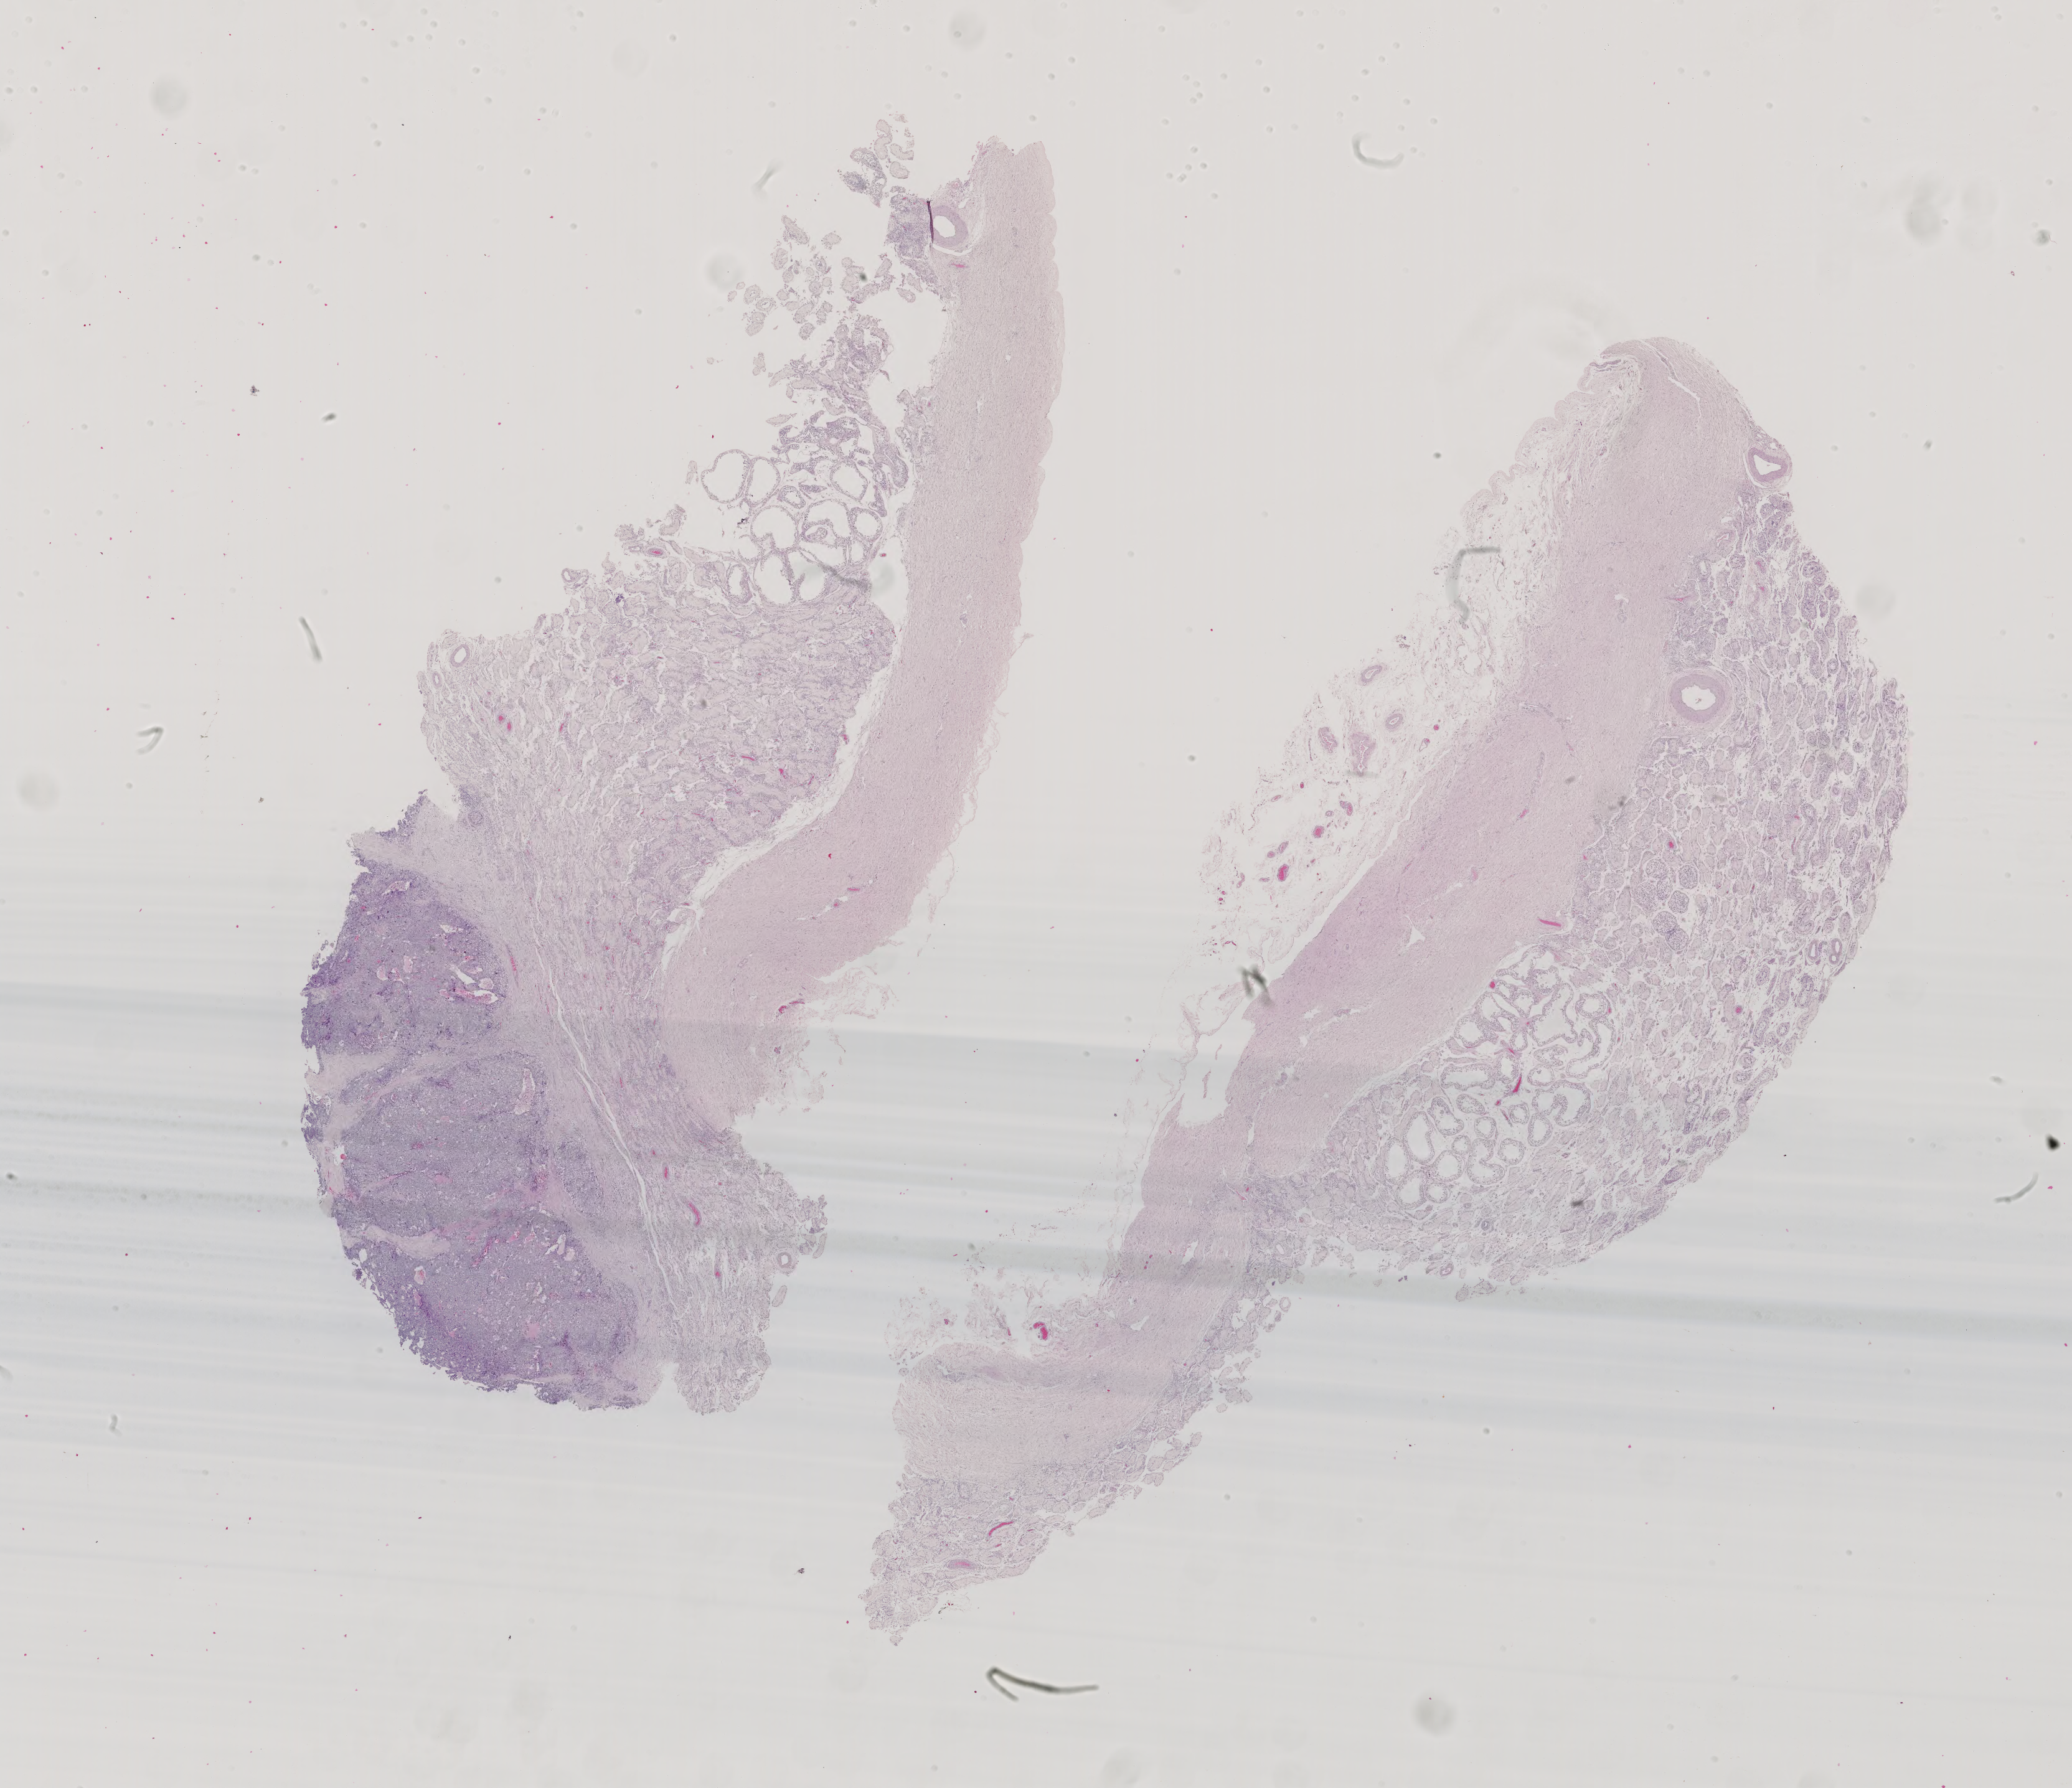
Digitized H&E-stained tissue section (whole slide), shown as a low-resolution overview of the whole scanned area (about 24.2 x 20.9 mm, acquisition: 40x scan), formalin-fixed paraffin-embedded (FFPE) diagnostic section, sample: primary tumour, testis. Male patient; age at initial diagnosis 38 years.
Diagnosis: Embryonal carcinoma, NOS. Laterality: right. TNM: T1 N1 M0. AJCC pathologic stage: IIA (6th edition).